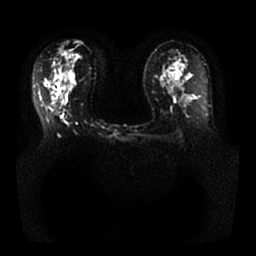
Breast MRI, one axial slice. Position 13 of 25 along the scan axis. Diffusion-weighted series; image 2 of 4 stored at this slice position (different b-values; order by instance number). 1.5 T. 4 mm slice thickness. 256 × 256 image matrix, field of view 350 × 350 mm. Female patient.
Outlined on this slice (outlined manually by an expert reader):
- tumour on diffusion-weighted imaging: box from (x=54, y=102) to (x=62, y=112) px